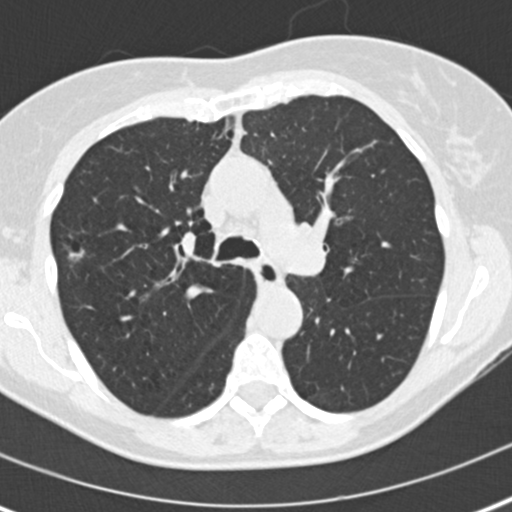
Low-dose screening chest CT, axial slice. Second annual screen. Lung window (W 1500 / L -600 HU). 2 mm slice thickness. 120 kVp. Slice 68 of 186 in the series. Female participant, aged 60 years at enrolment. Current smoker at enrolment.
- Lesion marked by an expert reader, box from (x=50, y=229) to (x=100, y=276) px.
- Screening reader's record for this exam (one nodule recorded; not confirmed to be the boxed lesion): non-calcified nodule or mass ≥4 mm, right upper lobe, 8 × 6 mm, spiculated (stellate) margins, soft tissue attenuation, pre-existing on the prior screen: no.
- Official screen result: positive, other.
- Lung cancer was diagnosed 511 days after this screen (after the third annual screen): bronchiolo-alveolar adenocarcinoma, NOS, right upper lobe, well differentiated (G1), stage IA (AJCC 6th edition), 11 mm at pathology.